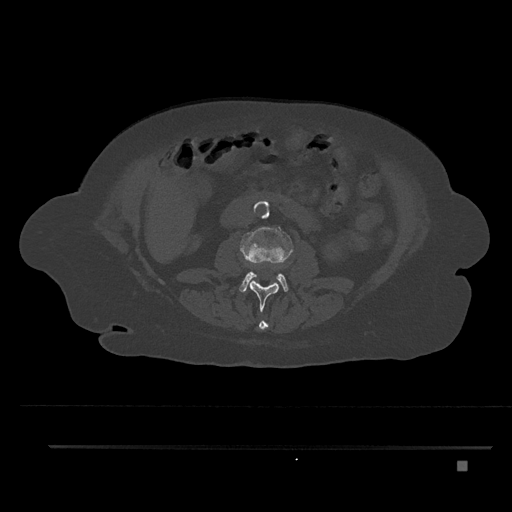
CT including the spine, one axial slice. Slice 158 of 797 in the series (ordered by position). Reconstruction kernel Br40s/3. Bone window (W 1800 / L 400 HU). 512 × 512 image matrix, field of view 437 × 437 mm. Female patient, age 76 years. Case-level facts recorded for this patient, not image findings: primary cancer: lung; vertebrae with lytic lesions (as recorded): T11, L3.
Structures marked on this image (semi-automatic segmentation, software-assisted and operator-edited):
- L1 vertebra: bounding box (x1, y1, x2, y2) in pixels: (259, 321, 269, 331)
- L2 vertebra: (248, 265, 279, 312)
- L3 vertebra: (240, 226, 294, 292)